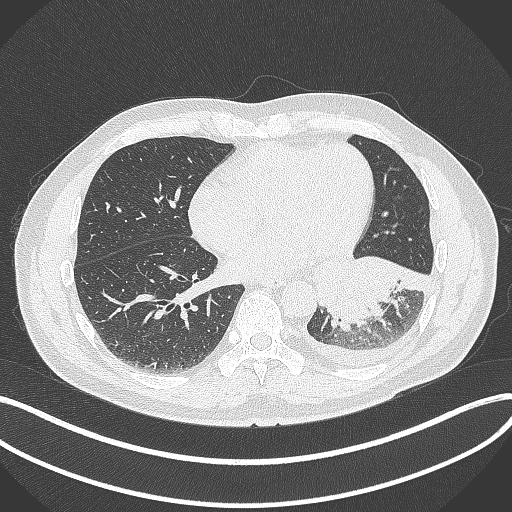
Chest CT, one axial slice; 120 kVp; lung window (W 1500 / L -600 HU); 1 mm slice thickness; 512 × 512 image matrix. Patient: male, 58 years. From the clinical record (not read from this slice): clinical TNM (as recorded): T3 N1 M1b; histopathological grade: G3.
Structures marked on this image (rectangle marked by the reading radiologist):
- lung tumour (recorded histology: small cell carcinoma): bounding box (x1, y1, x2, y2) in pixels: (303, 247, 430, 331)